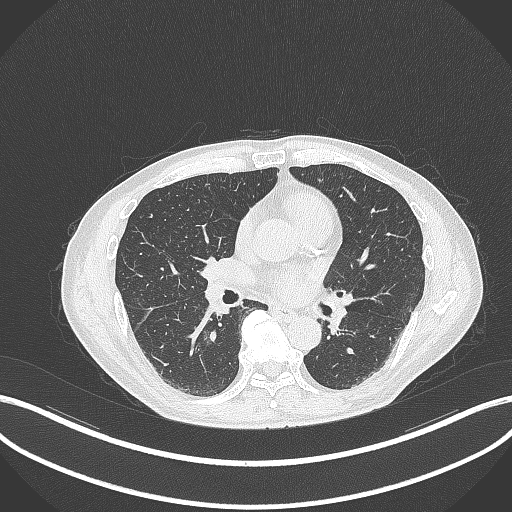
Chest CT, one axial slice; position 160 of 323 along the scan axis; 120 kVp; lung window (W 1500 / L -600 HU); 1 mm slice thickness; 512 × 512 image matrix, field of view 400 × 400 mm. Patient: male, 61 years. Case-level facts recorded for this patient, not image findings: clinical TNM (as recorded): T1c N0 M0.
Annotated regions visible in this slice (bounding box drawn by a radiologist):
- lung tumour (recorded histology: adenocarcinoma): box from (x=201, y=325) to (x=213, y=347) px